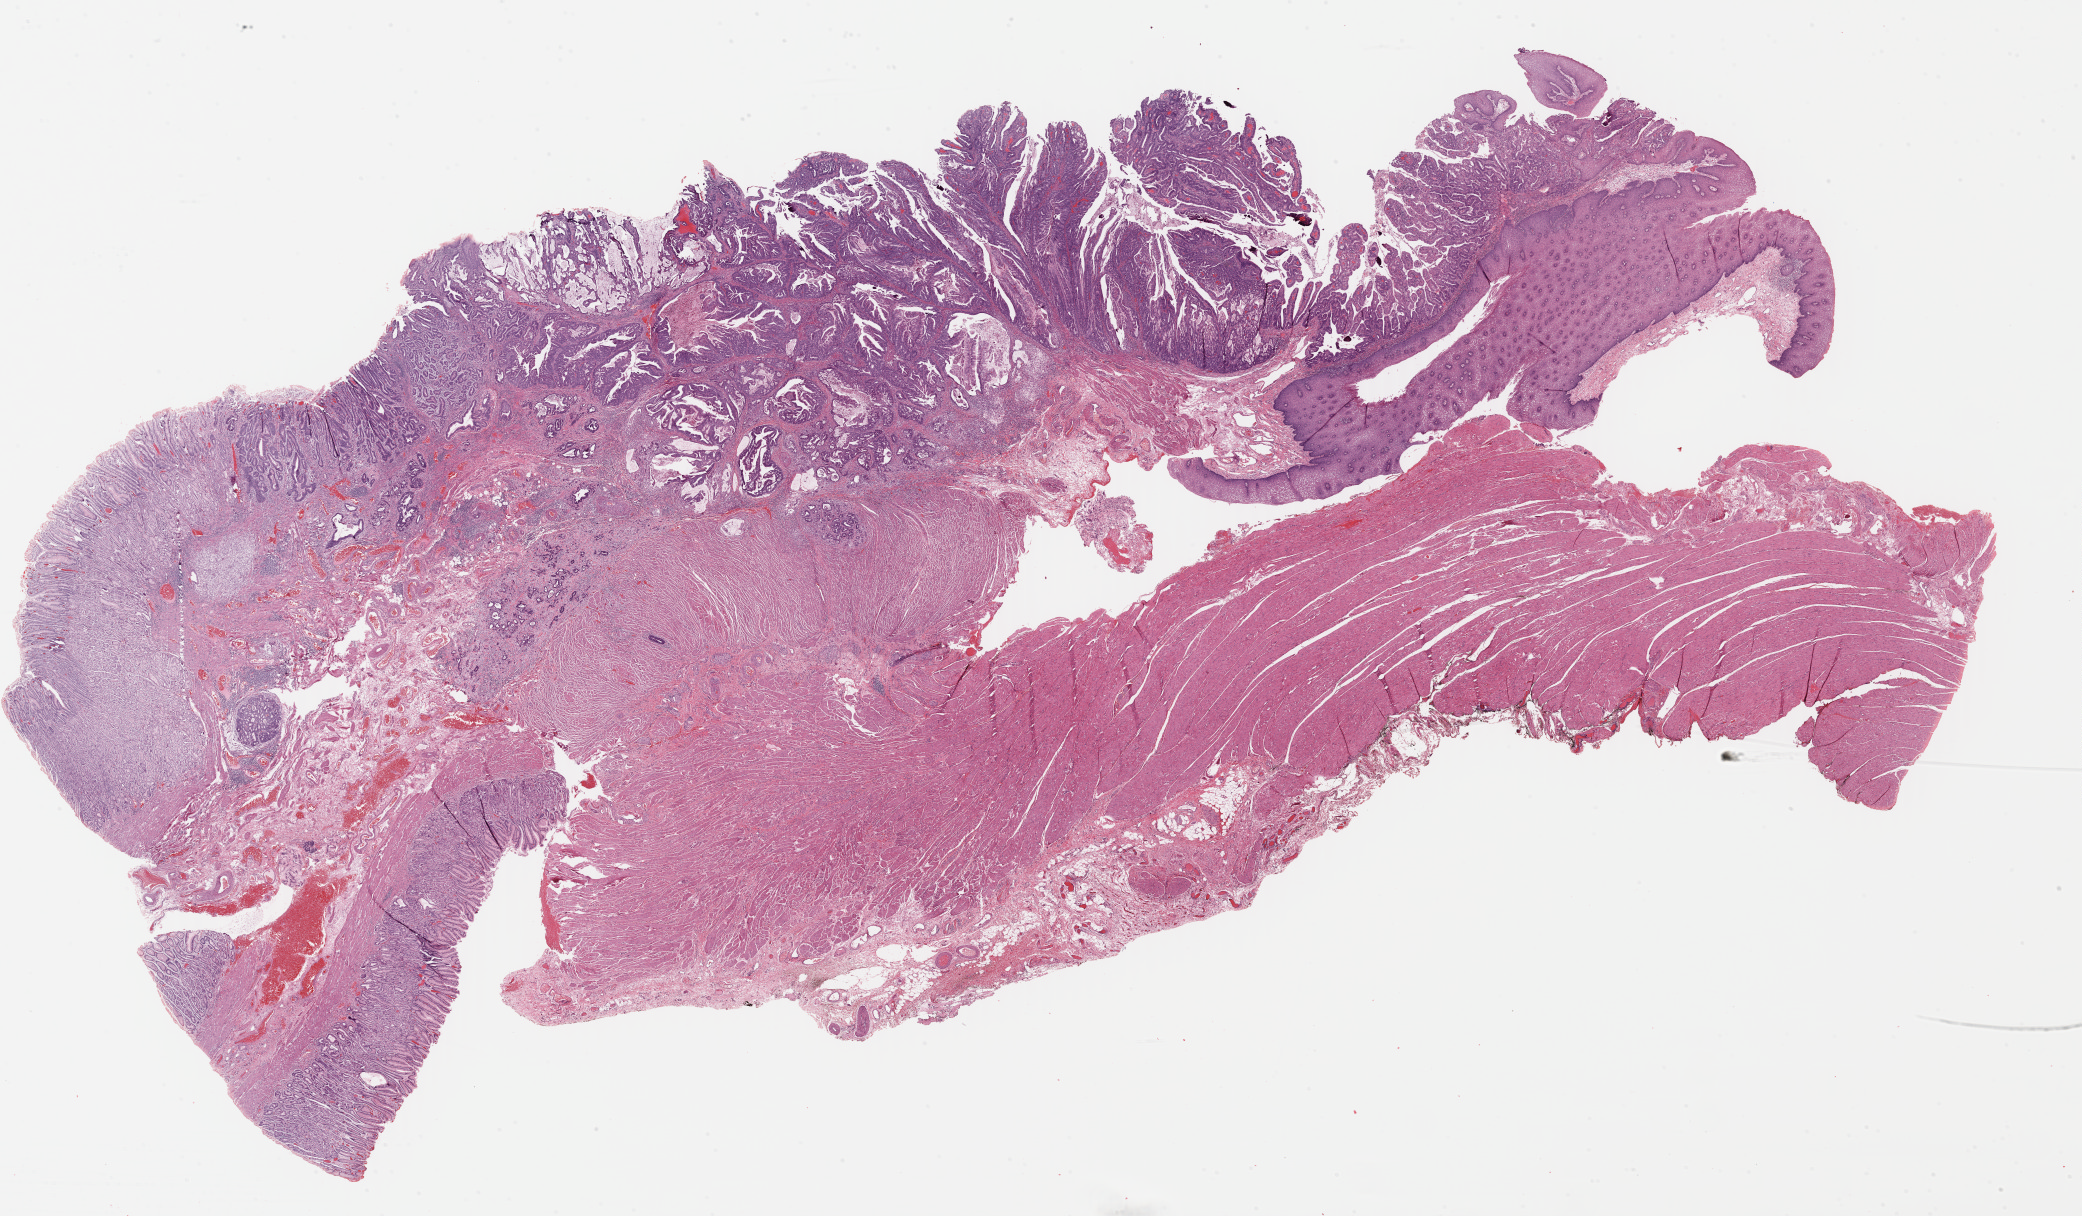
Whole-slide histology image, Hematoxylin and eosin (H&E) stained, shown as a low-resolution overview of the whole scanned area (about 32.7 x 19.1 mm). FFPE section. Primary tumour sample from the esophagus. Female patient; age at initial diagnosis 56 years. Histologic grade: GX (grade cannot be assessed).
- AJCC pathologic stage: IIB (6th edition)
- histologic diagnosis: Adenocarcinoma, NOS